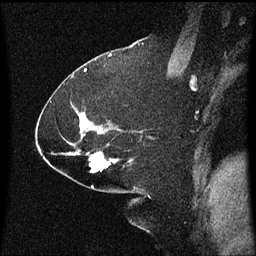
Breast MRI (dynamic contrast-enhanced), one sagittal slice; slice 34 of 60 in the series (ordered by position); dynamic contrast-enhanced series, image 2 of 3 at this slice position (ordered by acquisition); 1.5 T; TE 4.2 ms, TR 8 ms; 256 × 256 image matrix, field of view 200 × 200 mm. Female patient, age 59 years.
Structures marked on this image (semi-automatically segmented with operator editing):
- analysis volume of interest (the breast-tissue region the enhancement analysis was run in; not a lesion): bounding box (x1, y1, x2, y2) in pixels: (86, 152, 131, 173)
- tumour enhancement mask (voxels above the 70 % enhancement threshold inside the analysis volume of interest): (90, 152, 117, 173)